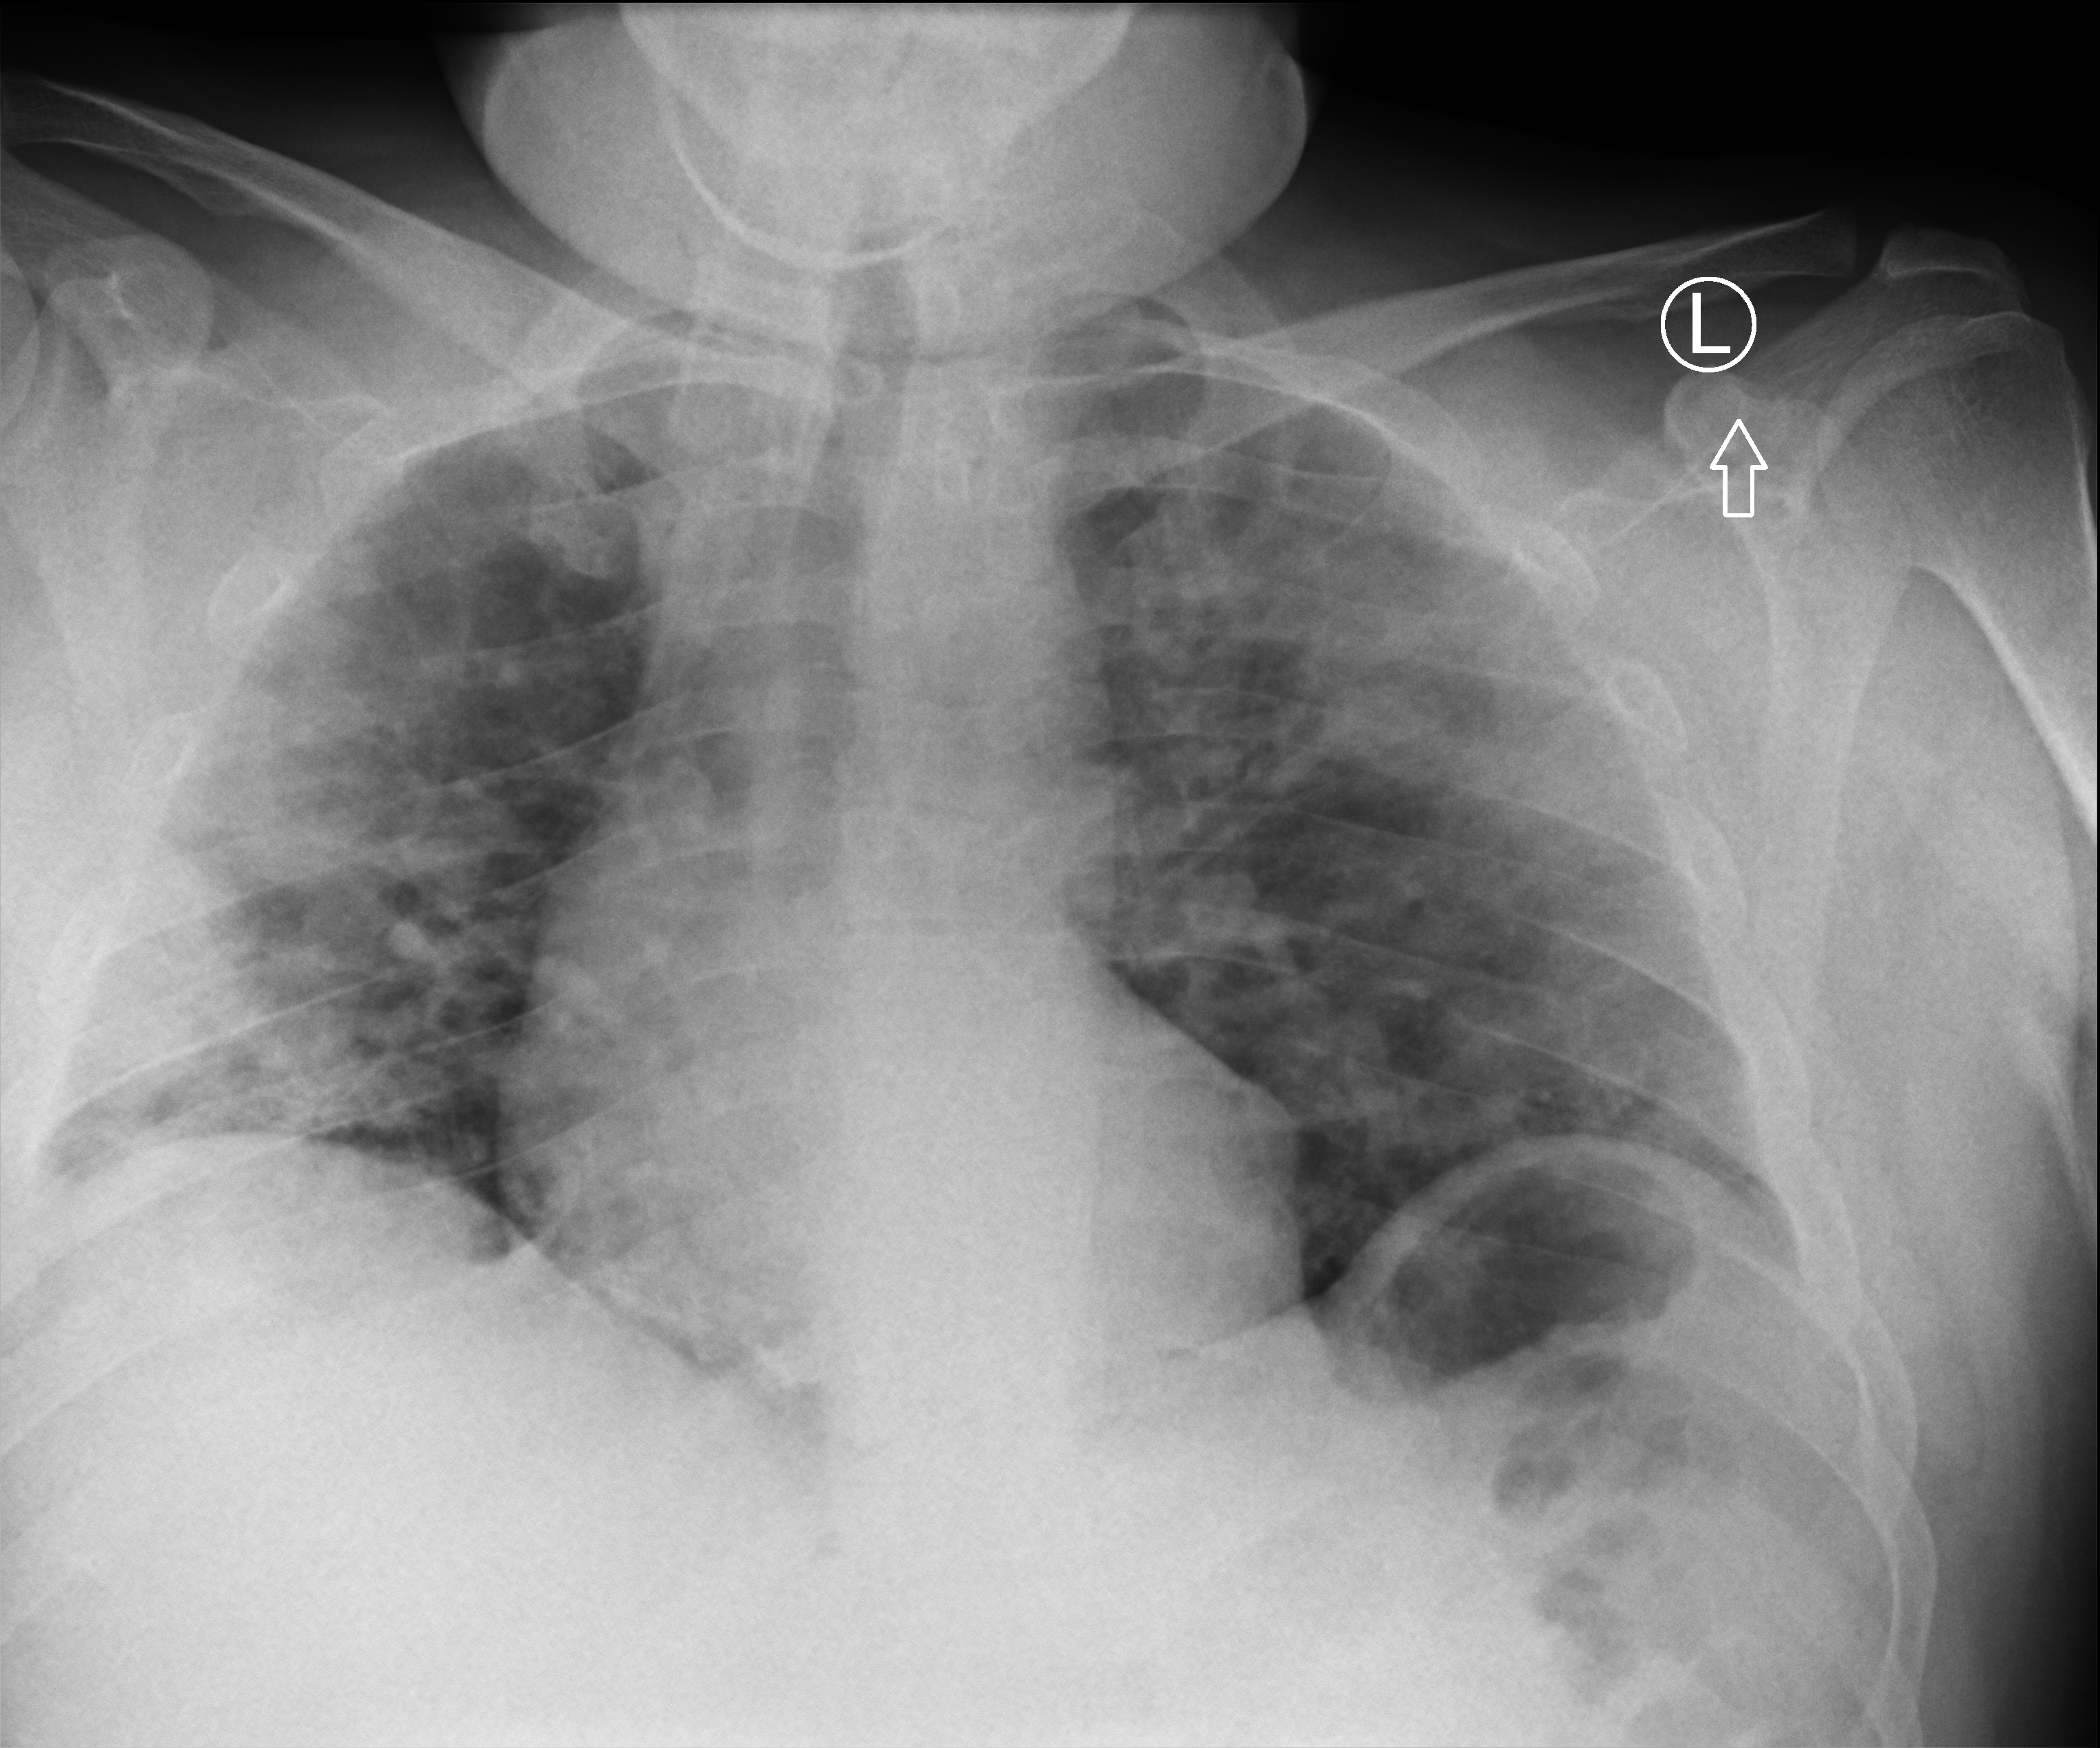
Portable chest radiograph; anteroposterior (AP) projection. Patient hospitalised with COVID-19; female, aged 18–59 years.
Hospital-stay facts (about this admission, not read from this image; timing relative to this image not recorded):
- admitted to intensive care during this hospital stay: yes